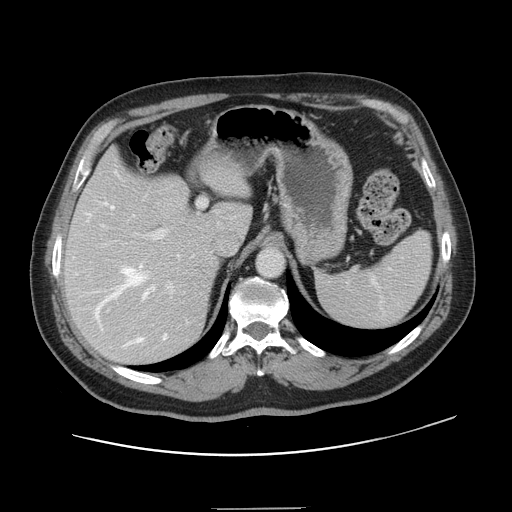
Contrast-enhanced abdominal CT, one axial slice. 120 kVp. Soft-tissue window (W 400 / L 40 HU). 512 × 512 image matrix, field of view 402 × 402 mm. Male patient, age 62 years. From the clinical record (not read from this slice): diagnosis: colorectal cancer liver metastases, imaged before liver resection; multiple liver metastases: yes; largest metastasis: 2.7 cm; disease in both lobes: no.
Annotated regions visible in this slice (manually delineated by an expert):
- hepatic veins: bounding box [x1, y1, x2, y2] px = [87, 174, 193, 344]
- liver: [65, 152, 250, 363]
- planned liver remnant (the part of the liver to remain after resection): [64, 152, 250, 259]
- portal vein (with intrahepatic branches): [90, 200, 206, 347]